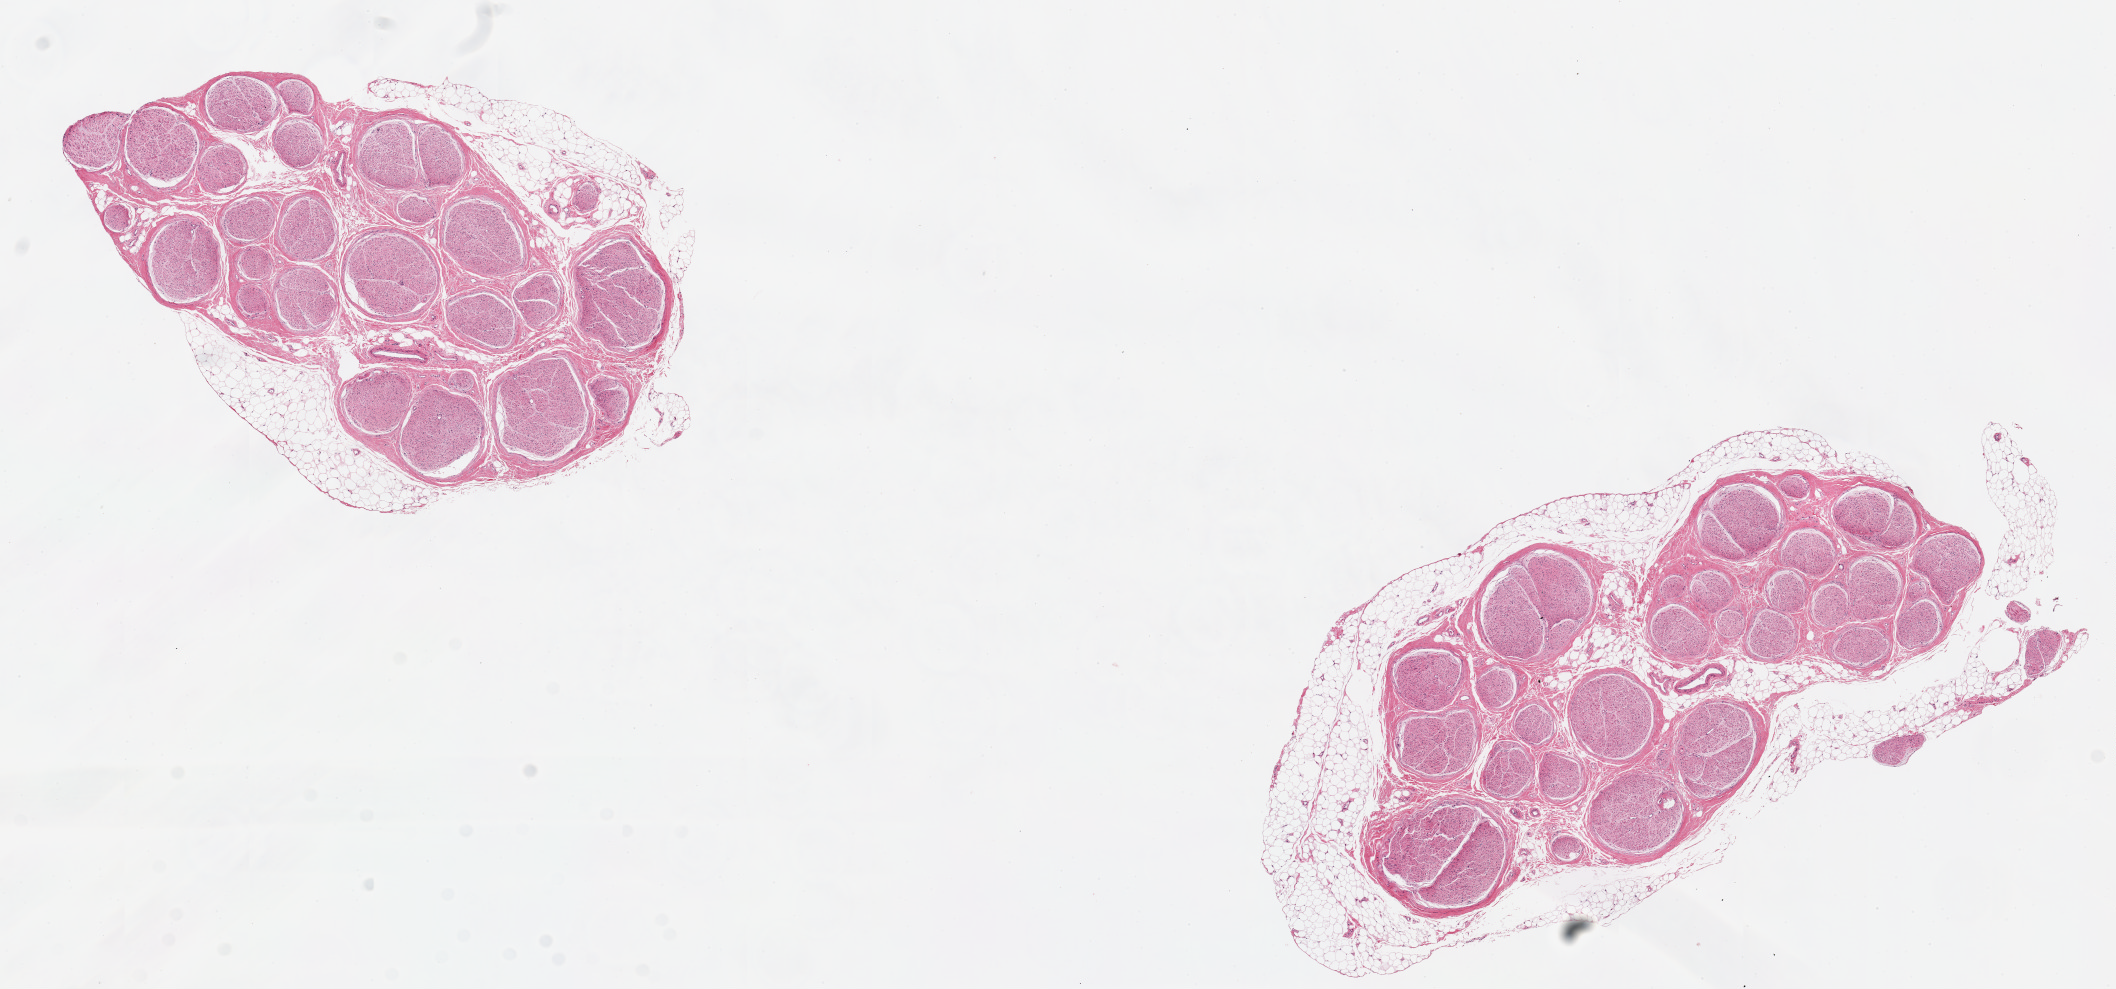
Digitized hematoxylin and eosin (H&E)-stained section, whole scanned area (about 16.7 x 7.8 mm) shown as a low-resolution overview. PAXgene-fixed, paraffin-embedded tissue. Sampled site (target tissue): tibial nerve. Tissue donor sample. Donor: female.
* pathologist's review note for this sample: 2 pieces, 5x4 & 7x3mm; 20% peripheral adipose